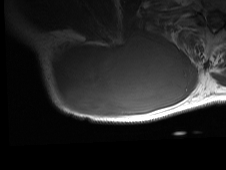
MRI of an extremity soft-tissue mass, one axial slice; position 46 of 81 along the scan axis; MR volume resampled by the dataset authors to the PET/CT grid (not the native acquisition matrix); 226 × 170 image matrix, field of view 221 × 166 mm. Male patient. From the clinical record (not read from this slice): histological type: pleiomorphic spindle cell undifferentiated; grade: high; site of the primary tumour: right parascapusular.
Structures marked on this image (expert contour drawn on MRI and transferred to this co-registered scan by the dataset authors):
- gross tumour volume including surrounding oedema: bounding box <48,31,198,117> (left, top, right, bottom; pixels)
- gross tumour volume (mass): <51,31,189,114>